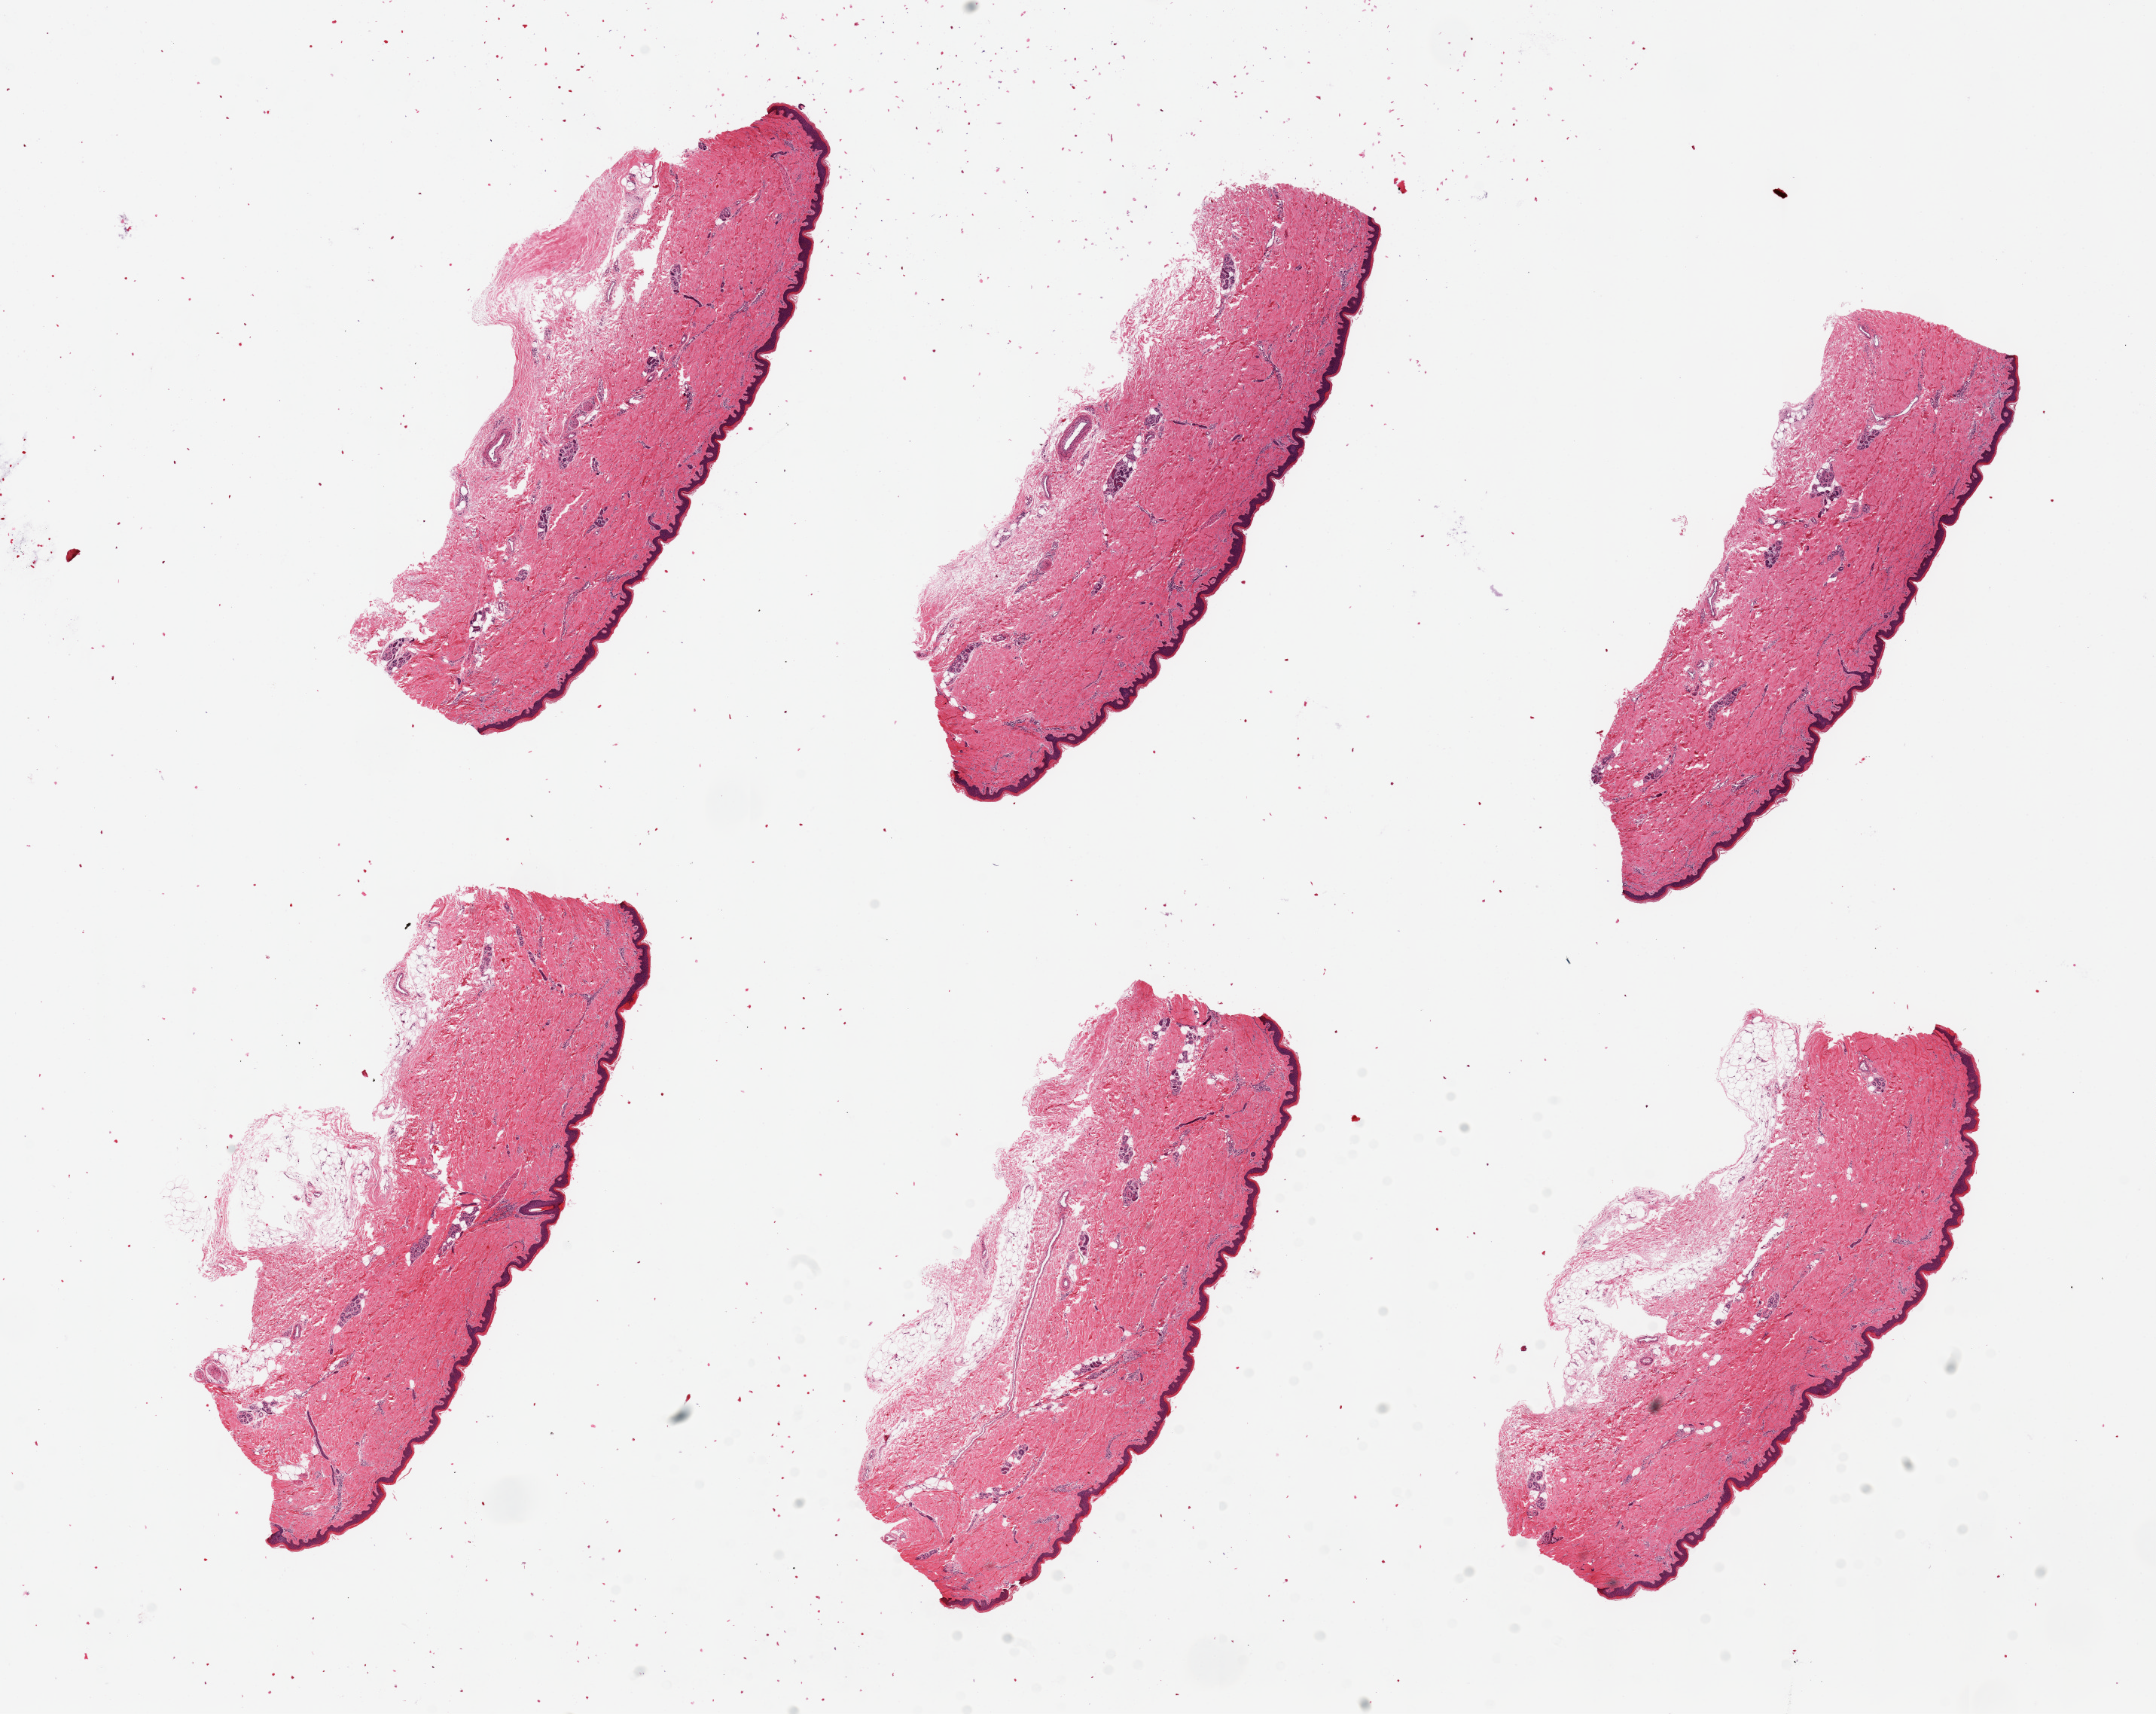
Whole-slide image, H&E stain, shown as a low-resolution overview of the whole scanned area (about 22.6 x 18.0 mm). PAXgene-fixed, paraffin-embedded tissue. Target tissue: skin of lower leg. Donor tissue sample. Donor: female.
Reviewer comment on this tissue sample: 6 pieces, up to 8x4mm; 3 with 1 mm subcutaneous adipose.